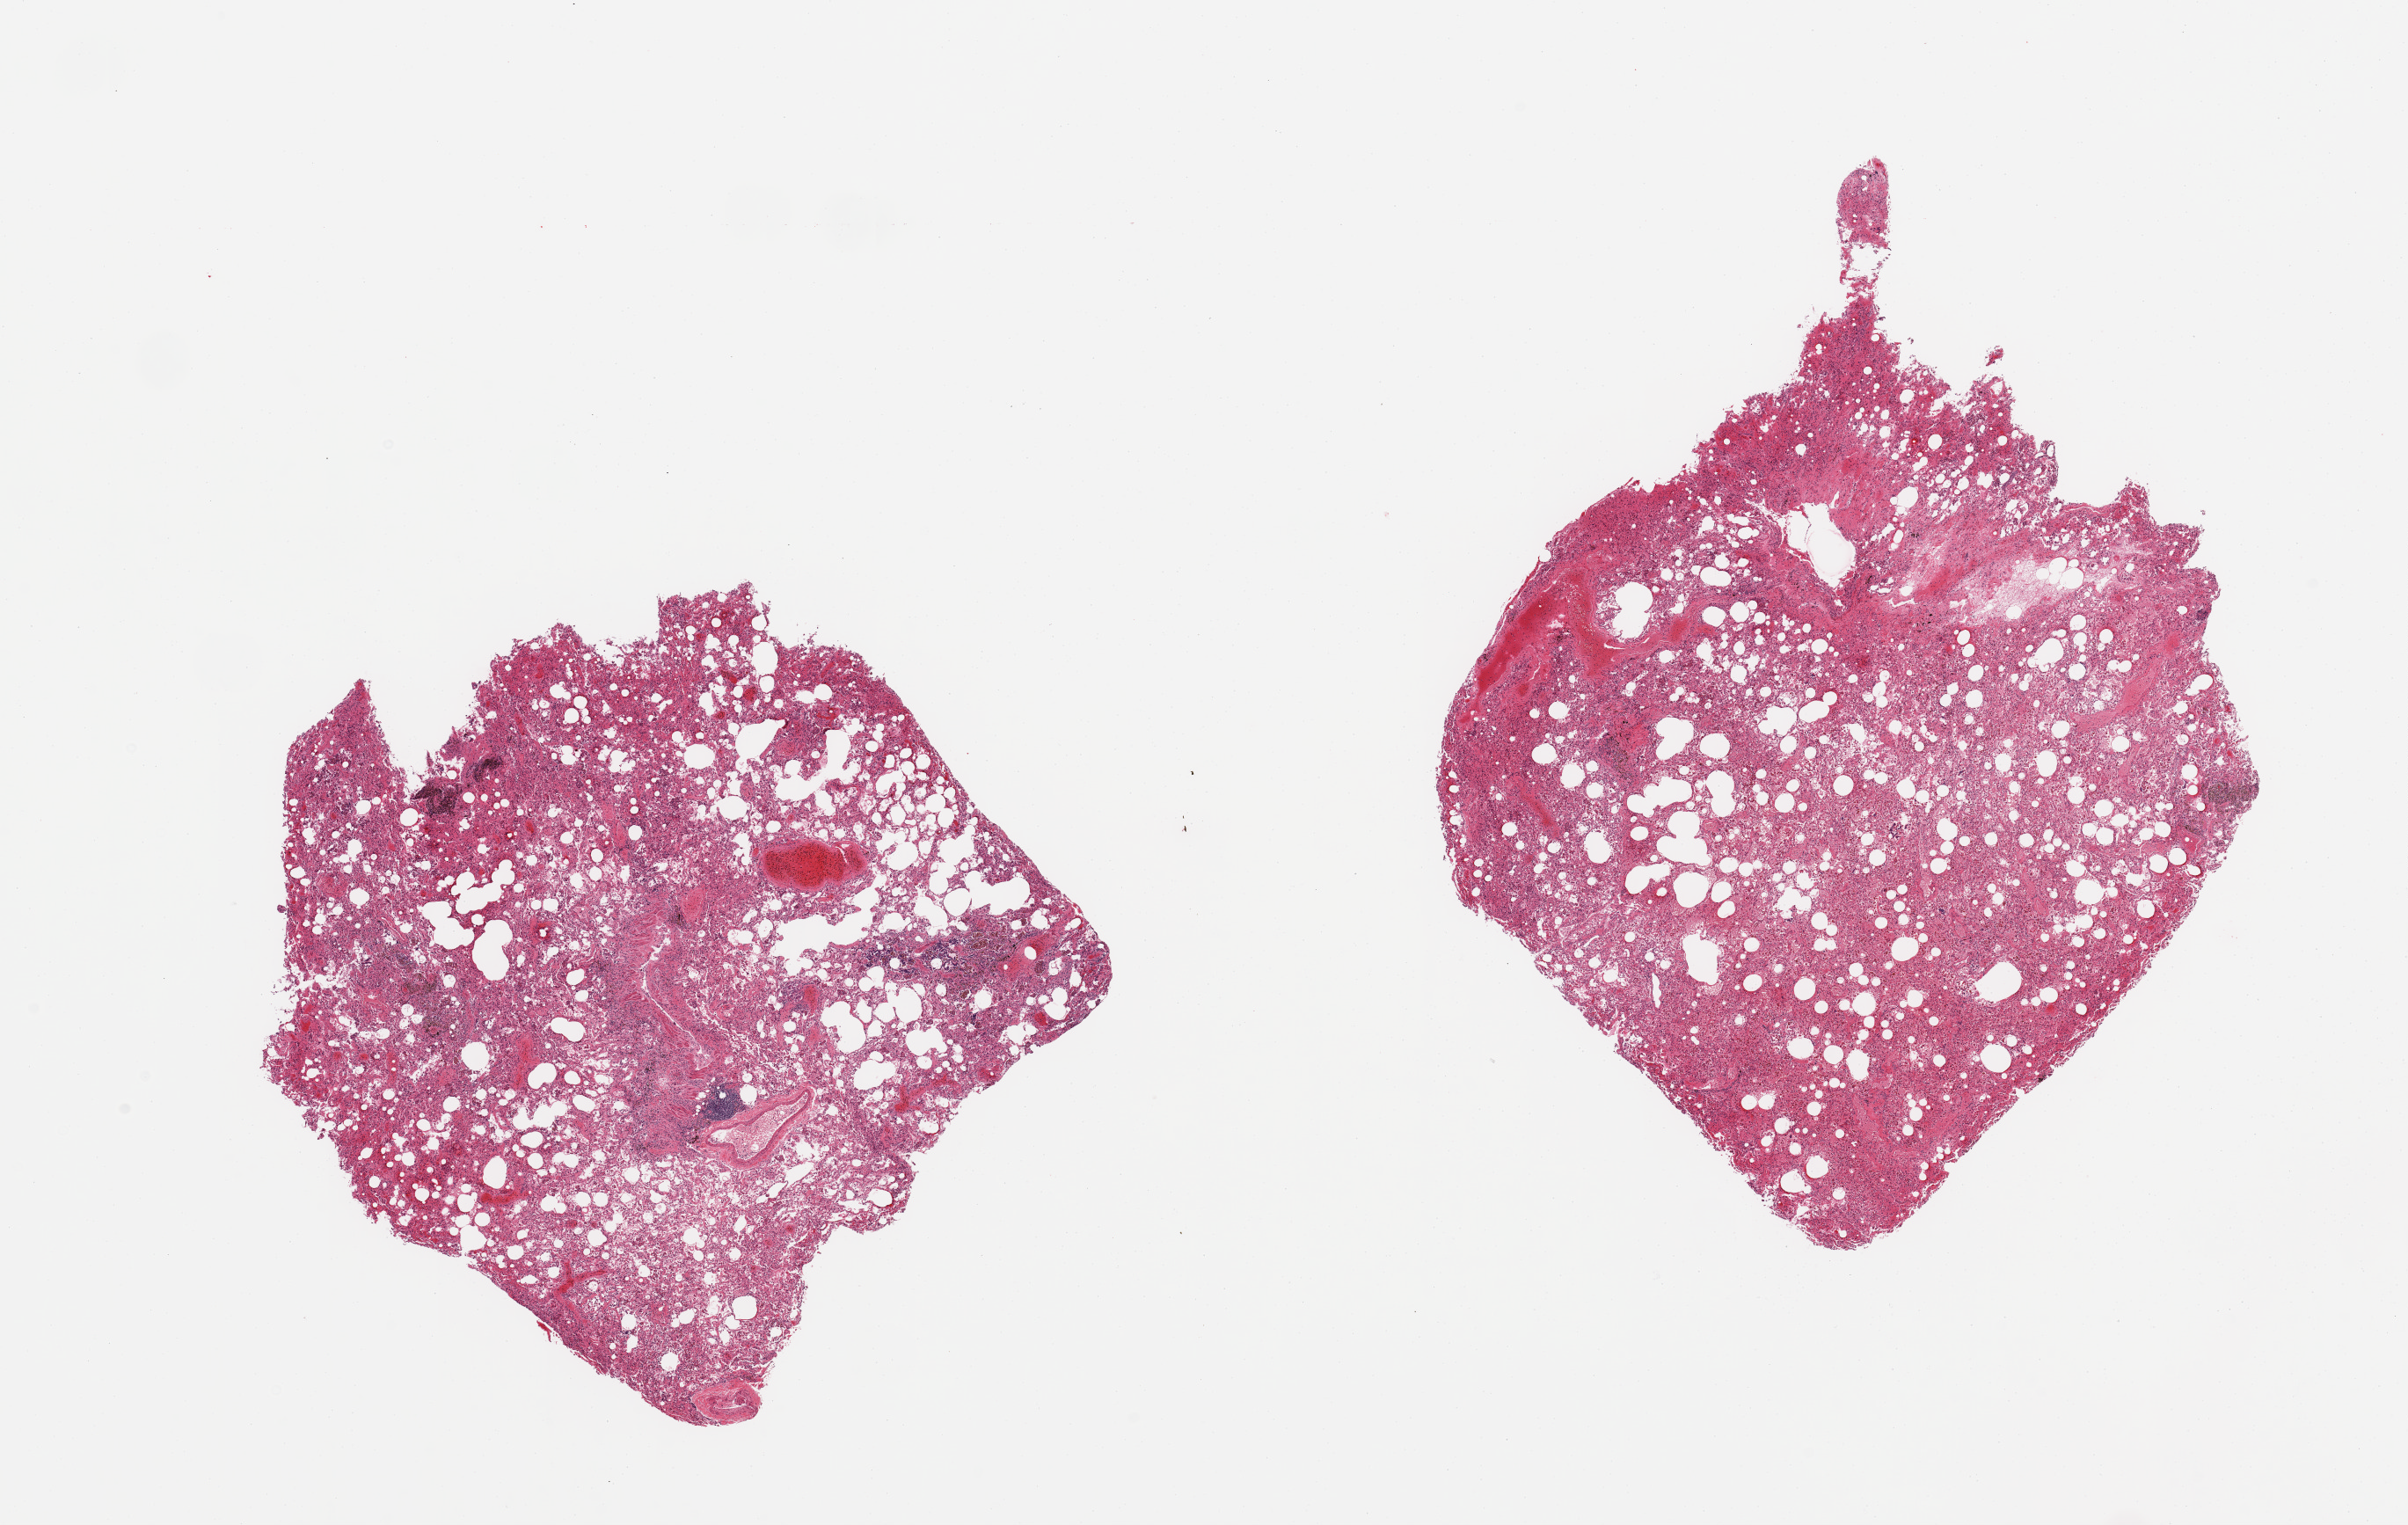
Whole-slide image, haematoxylin and eosin stain — low-resolution overview of the scanned area, about 21.7 x 13.7 mm (from a 20x scan), PAXgene-fixed paraffin-embedded (PFPE) section, sampled site (target tissue): lung, tissue donor sample.
Reviewer comment on this tissue sample: 2 pieces, marked acute/chronic congestion.